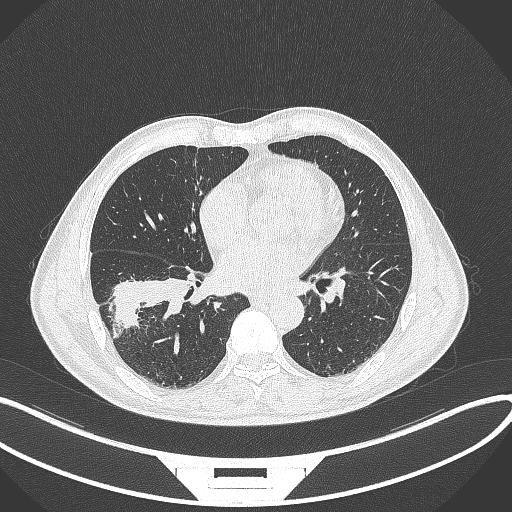
Chest CT, one axial slice. Slice 160 of 364 in the series (ordered by position). Lung window (W 1500 / L -600 HU). 1 mm slice thickness. 512 × 512 image matrix, field of view 400 × 400 mm. Male patient, age 58 years. Case-level facts recorded for this patient, not image findings: clinical TNM (as recorded): T3 N0 M0.
Annotated regions visible in this slice (rectangle marked by the reading radiologist):
- lung tumour (recorded histology: squamous cell carcinoma): bounding box <112,275,198,328> (left, top, right, bottom; pixels)